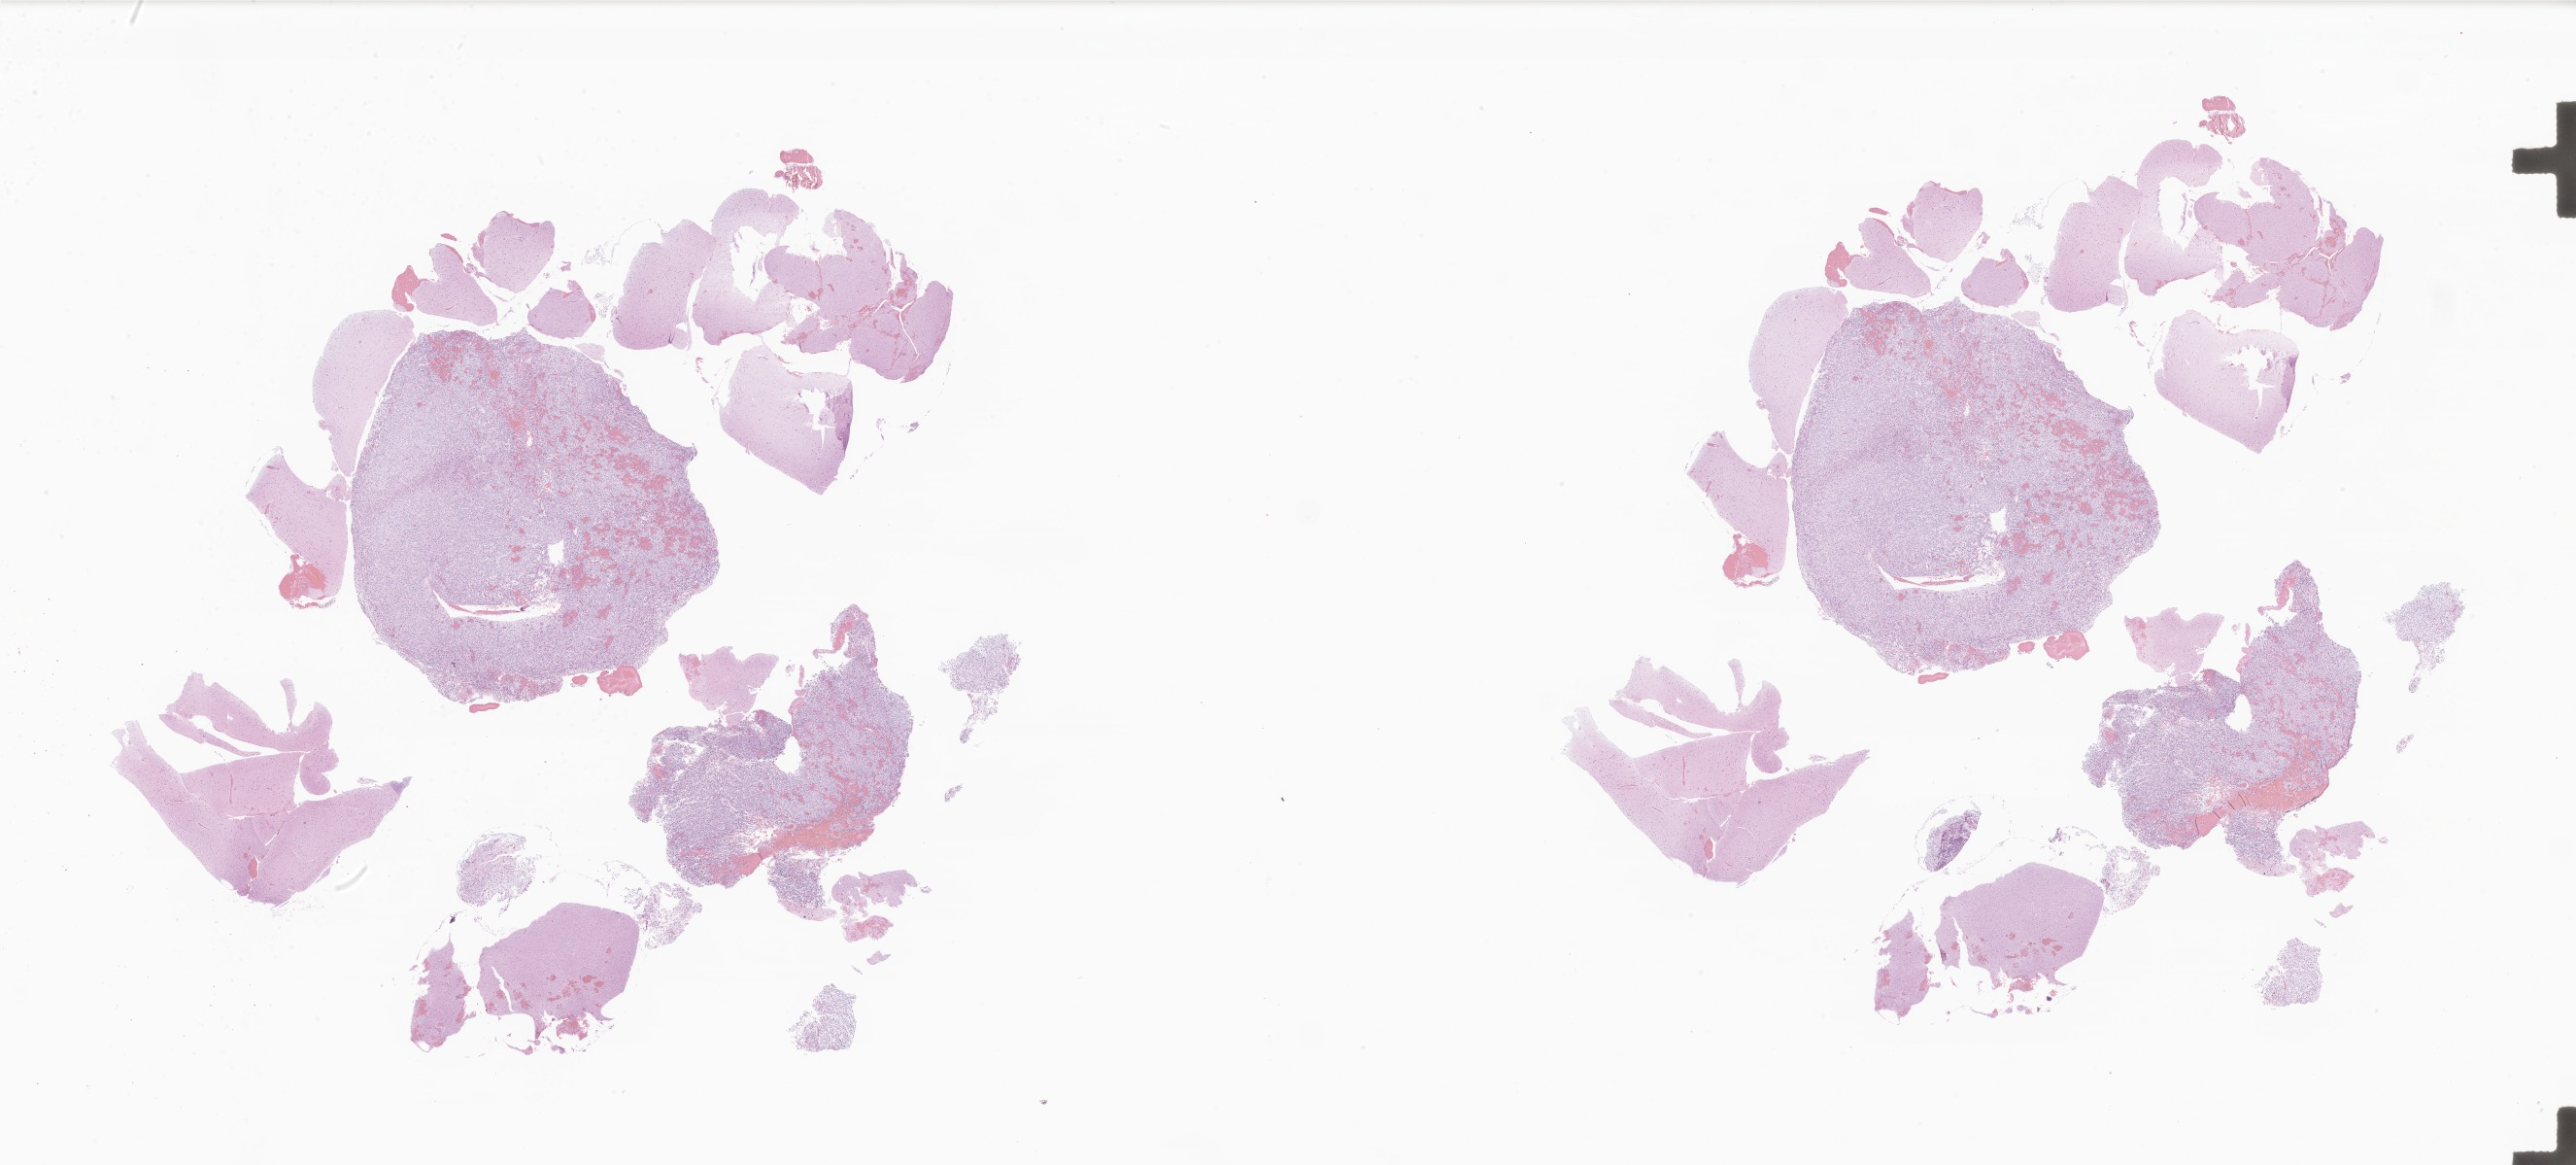
Whole-slide image, hematoxylin and eosin (H&E) stain of tumor tissue from the brain, low-resolution overview of the scanned area, about 44.7 x 20.2 mm, FFPE section. Patient: female, age 136 months (11 years 4 months).
* diagnosis (ICD-O-3 morphology term): Pilocytic astrocytoma